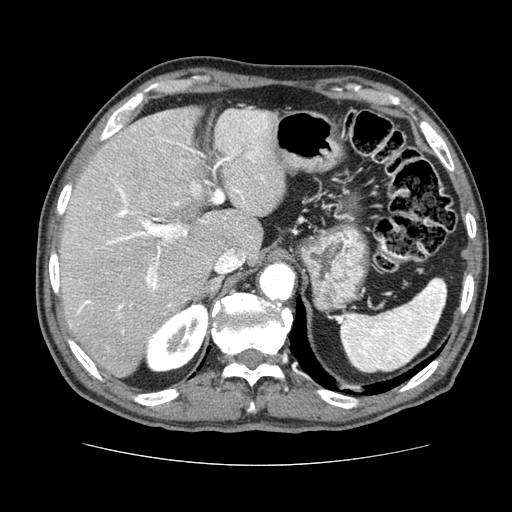
Contrast-enhanced abdominal CT (liver protocol), one axial slice; slice 50 of 79 in the series (ordered by position); 120 kVp; soft-tissue window (W 400 / L 40 HU); 2.5 mm slice thickness; 512 × 512 image matrix, field of view 360 × 360 mm. From the clinical record (not read from this slice): diagnosis: hepatocellular carcinoma (patient treated with transarterial chemoembolisation; whether this scan precedes or follows treatment is not stated here); TNM stage (as recorded): Stage-I; Child-Pugh class: A.
Outlined on this slice (semi-automatically segmented with operator editing):
- liver parenchyma outside the tumour (the mass and vessels are separate outlines, so this box may not span the whole liver): bounding box (x1, y1, x2, y2) in pixels: (60, 106, 284, 376)
- liver vessels: (77, 111, 268, 333)